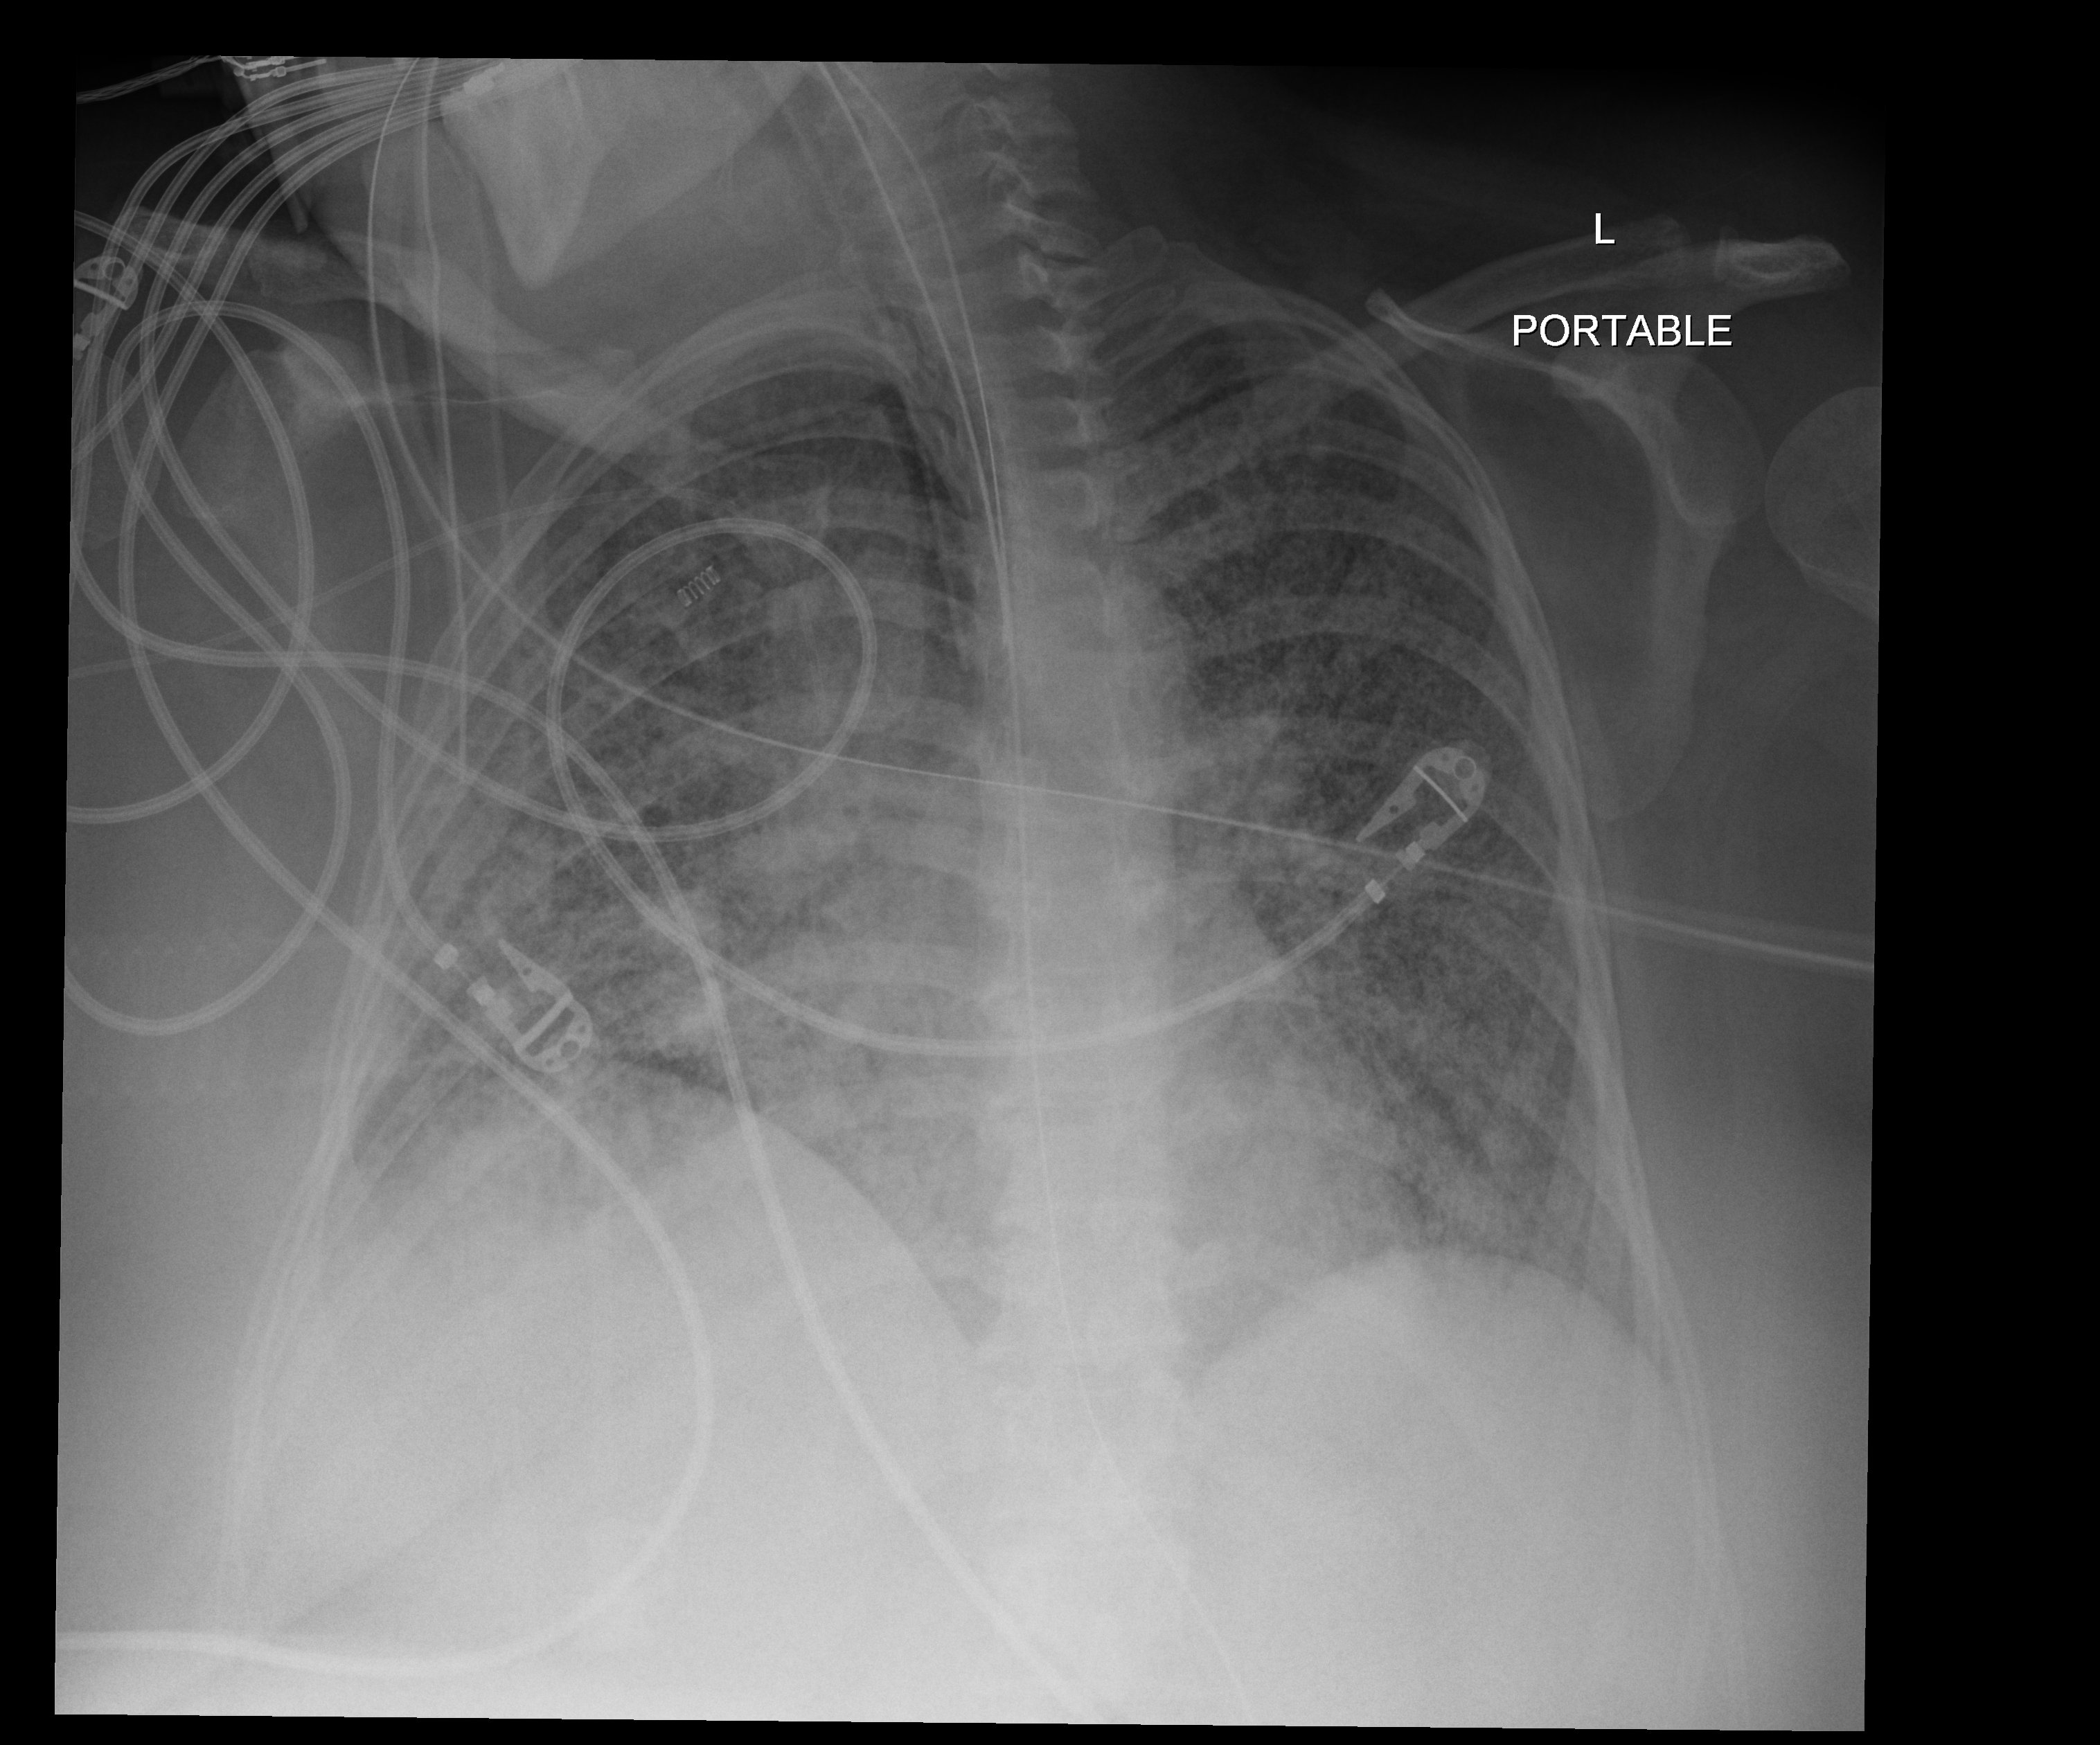
Chest X-ray (portable), anteroposterior (AP) projection. Female patient hospitalised with COVID-19, age 18–59 years.
Hospital-stay facts (about this admission, not read from this image; timing relative to this image not recorded):
- length of hospital stay: 95 days
- admitted to intensive care during this hospital stay: yes